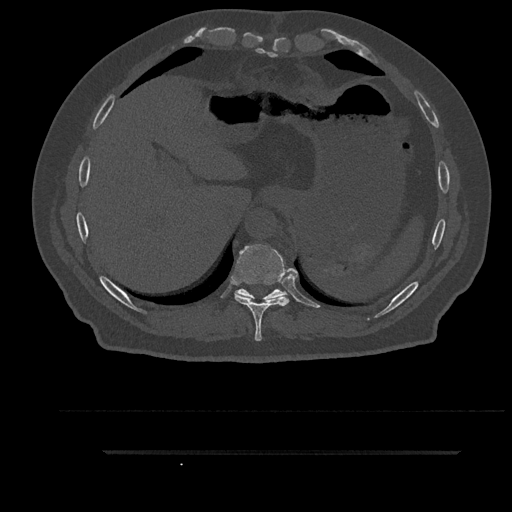
CT including the spine, one axial slice. Position 403 of 797 along the scan axis. Reconstruction kernel Br40s/3. 120 kVp. Bone window (W 1800 / L 400 HU). 0.5 mm slice thickness. 512 × 512 image matrix. Male patient, age 63 years. From the clinical record (not read from this slice): primary cancer: renal; vertebrae with lytic lesions (as recorded): T8.
Outlined on this slice (semi-automatically segmented with operator editing):
- T10 vertebra: bounding box (x1, y1, x2, y2) in pixels: (235, 288, 287, 300)
- T9 vertebra: (234, 244, 289, 341)